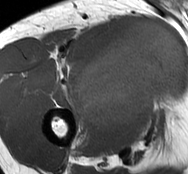
MRI of an extremity soft-tissue mass, one axial slice; position 54 of 93 along the scan axis; MR volume resampled by the dataset authors to the PET/CT grid (not the native acquisition matrix); 3.27 mm slice thickness; 188 × 174 image matrix, field of view 184 × 170 mm. Male patient. Case-level facts recorded for this patient, not image findings: histological type: undifferentiated - pleiomorphic; grade: high; site of the primary tumour: right thigh.
Annotated regions visible in this slice (expert contour drawn on MRI and transferred to this co-registered scan by the dataset authors):
- gross tumour volume including surrounding oedema: bounding box [x1, y1, x2, y2] px = [75, 21, 185, 129]
- gross tumour volume (mass): [75, 21, 185, 129]